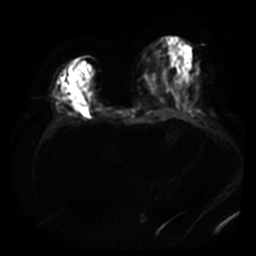
Breast MRI, one axial slice; slice 15 of 40 in the series (ordered by position); diffusion-weighted series; image 2 of 4 stored at this slice position (different b-values; order by instance number); 3 T; 5 mm slice thickness; 256 × 256 image matrix, field of view 380 × 380 mm. Female patient.
Annotated regions visible in this slice (expert manual segmentation):
- tumour on diffusion-weighted imaging: bounding box [x1, y1, x2, y2] px = [62, 95, 79, 106]